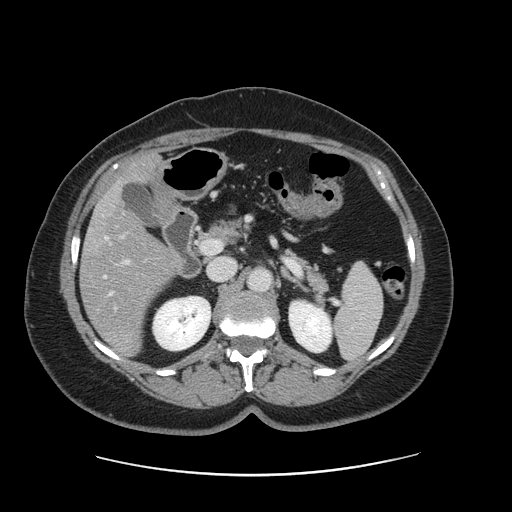
Contrast-enhanced abdominal CT, one axial slice. Slice 75 of 161 in the series (ordered by position). 120 kVp. Intravenous contrast given. Soft-tissue window (W 400 / L 40 HU). 2.5 mm slice thickness. 512 × 512 image matrix. Female patient, age 62 years. From the clinical record (not read from this slice): diagnosis: colorectal cancer liver metastases, imaged before liver resection; multiple liver metastases: no; largest metastasis: 2.5 cm; disease in both lobes: no.
Annotated regions visible in this slice (manually delineated by an expert):
- hepatic veins: box from (x=104, y=237) to (x=112, y=295) px
- liver: (x=82, y=157)–(x=178, y=356)
- planned liver remnant (the part of the liver to remain after resection): (x=117, y=157)–(x=158, y=188)
- portal vein (with intrahepatic branches): (x=120, y=235)–(x=129, y=264)